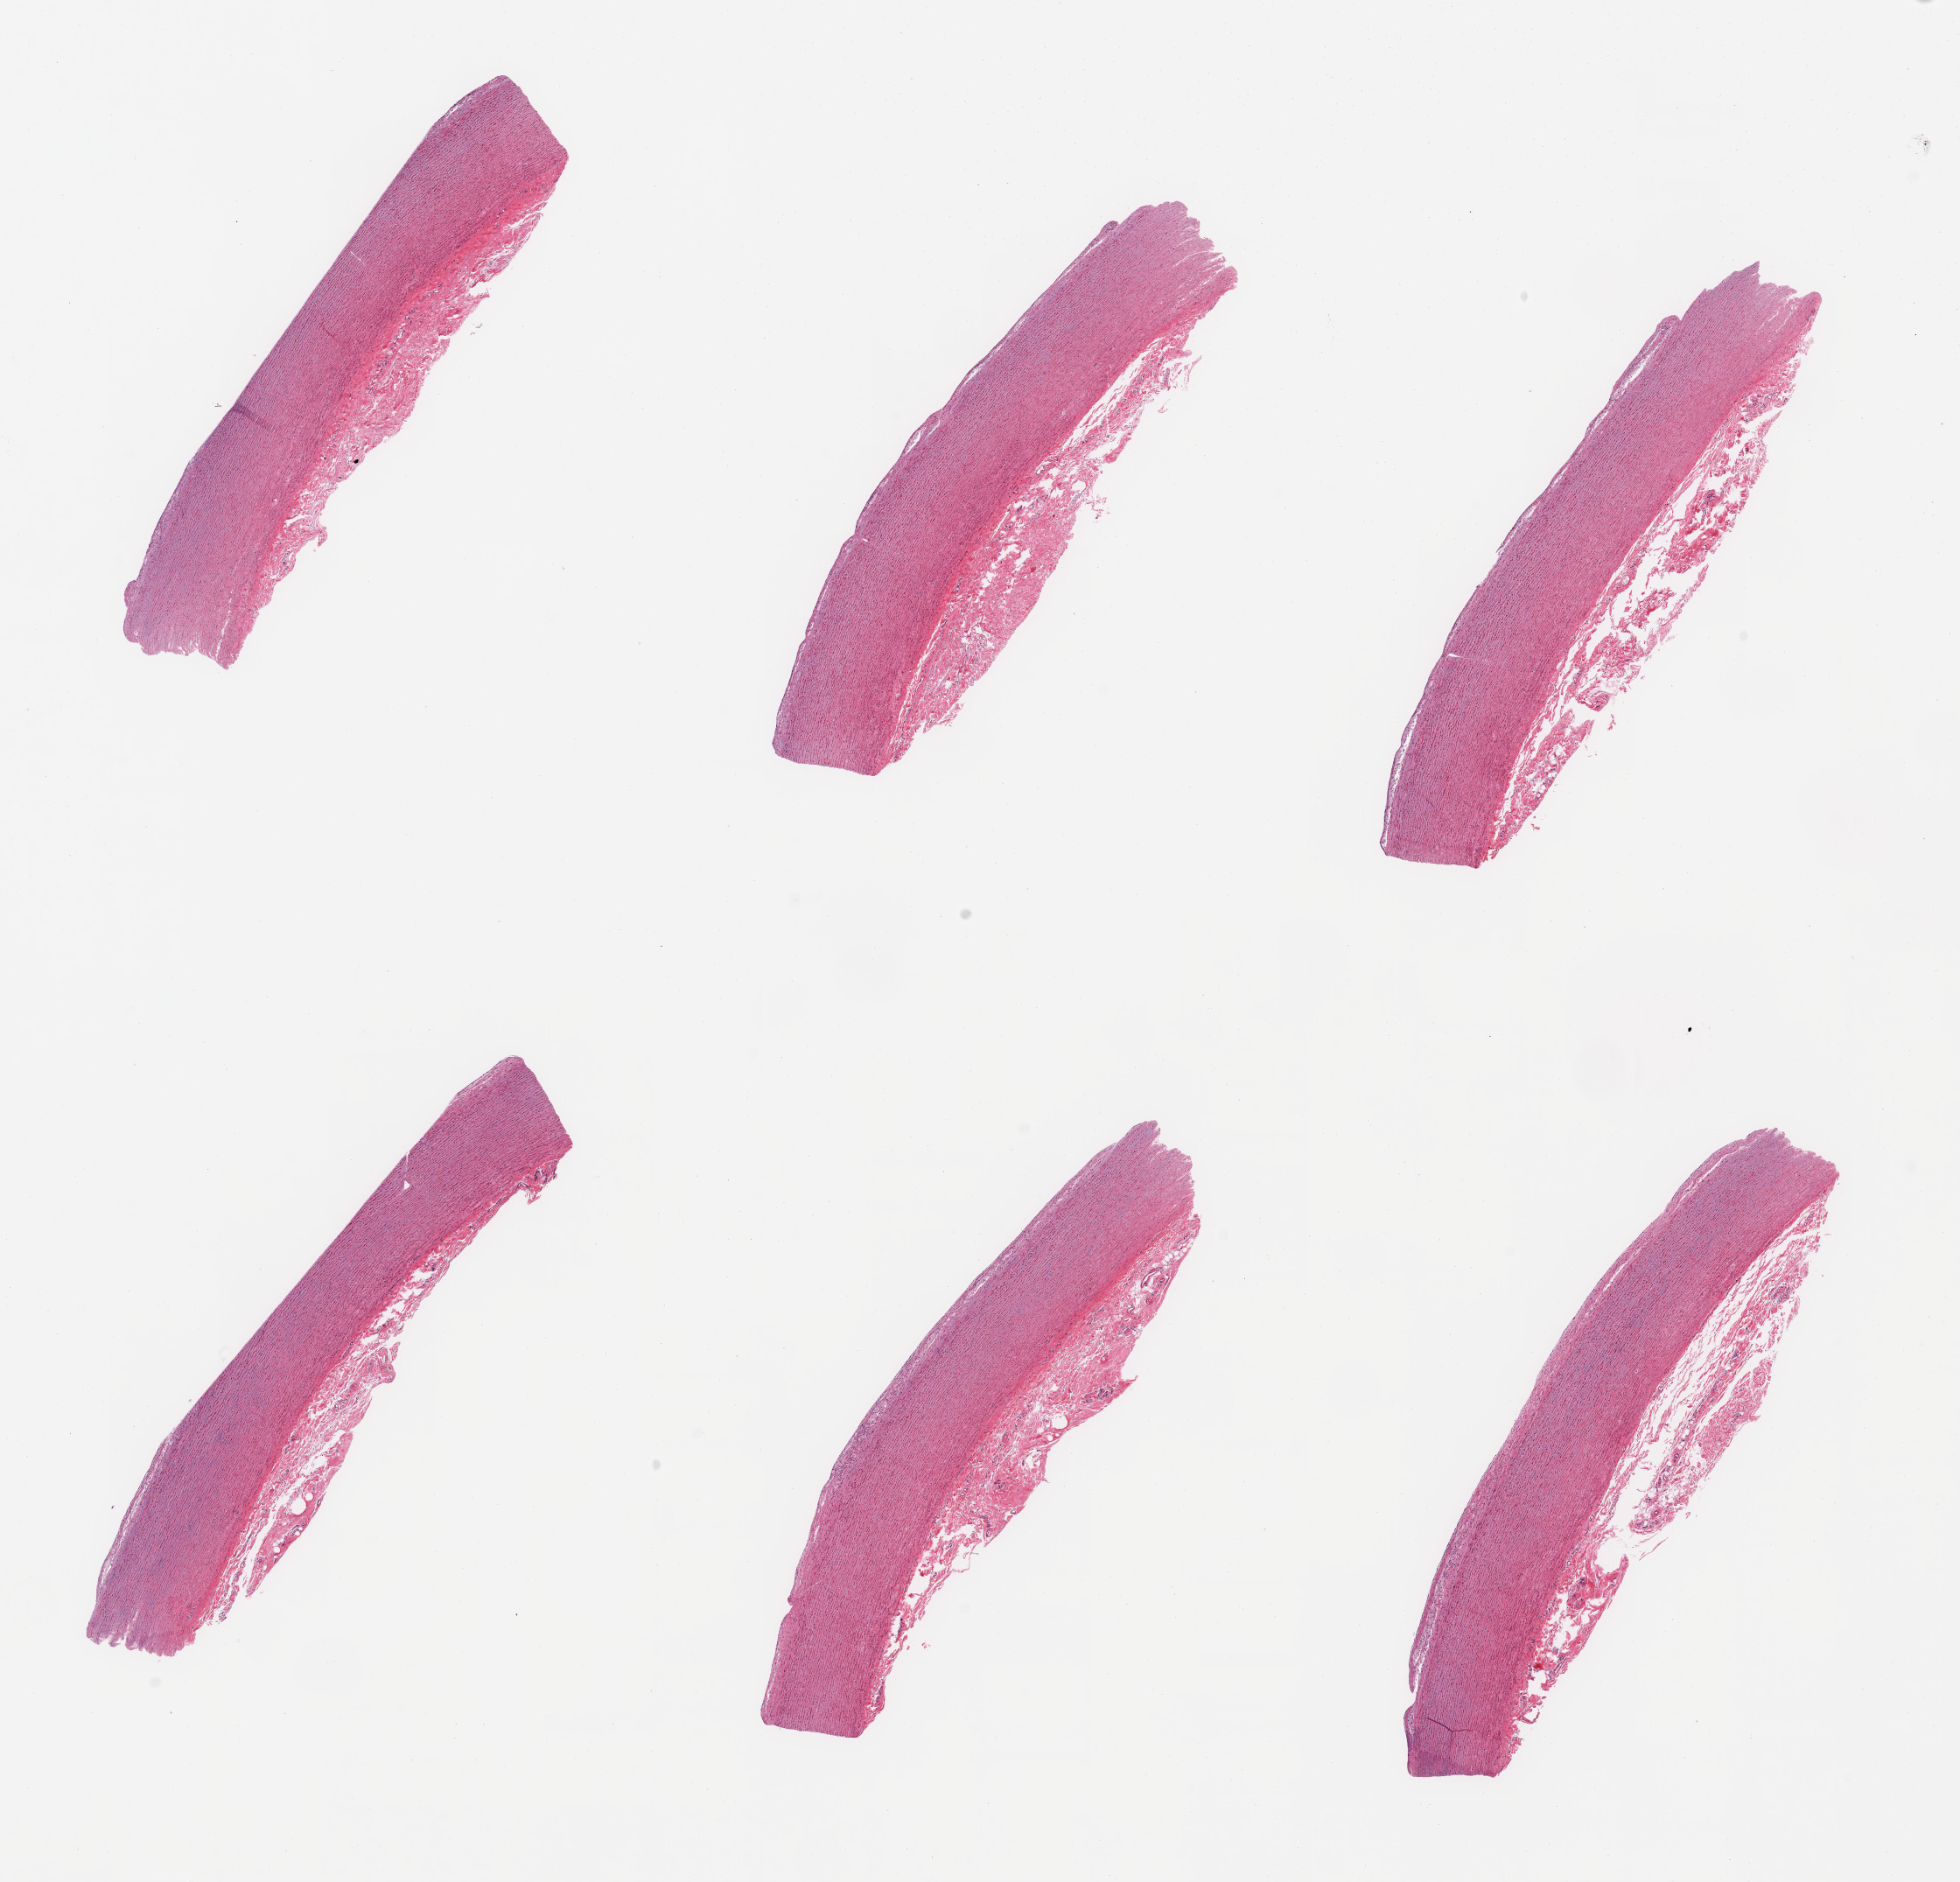
Whole-slide image, haematoxylin and eosin stain, low-resolution overview of the scanned area, about 17.7 x 17.0 mm (from a 20x scan); PAXgene-fixed paraffin-embedded (PFPE) section; sampled site (target tissue): aorta; donor tissue sample. Female donor.
Pathologist's review note for this sample: 6 pieces, trace atherosis, ~0.1mm.